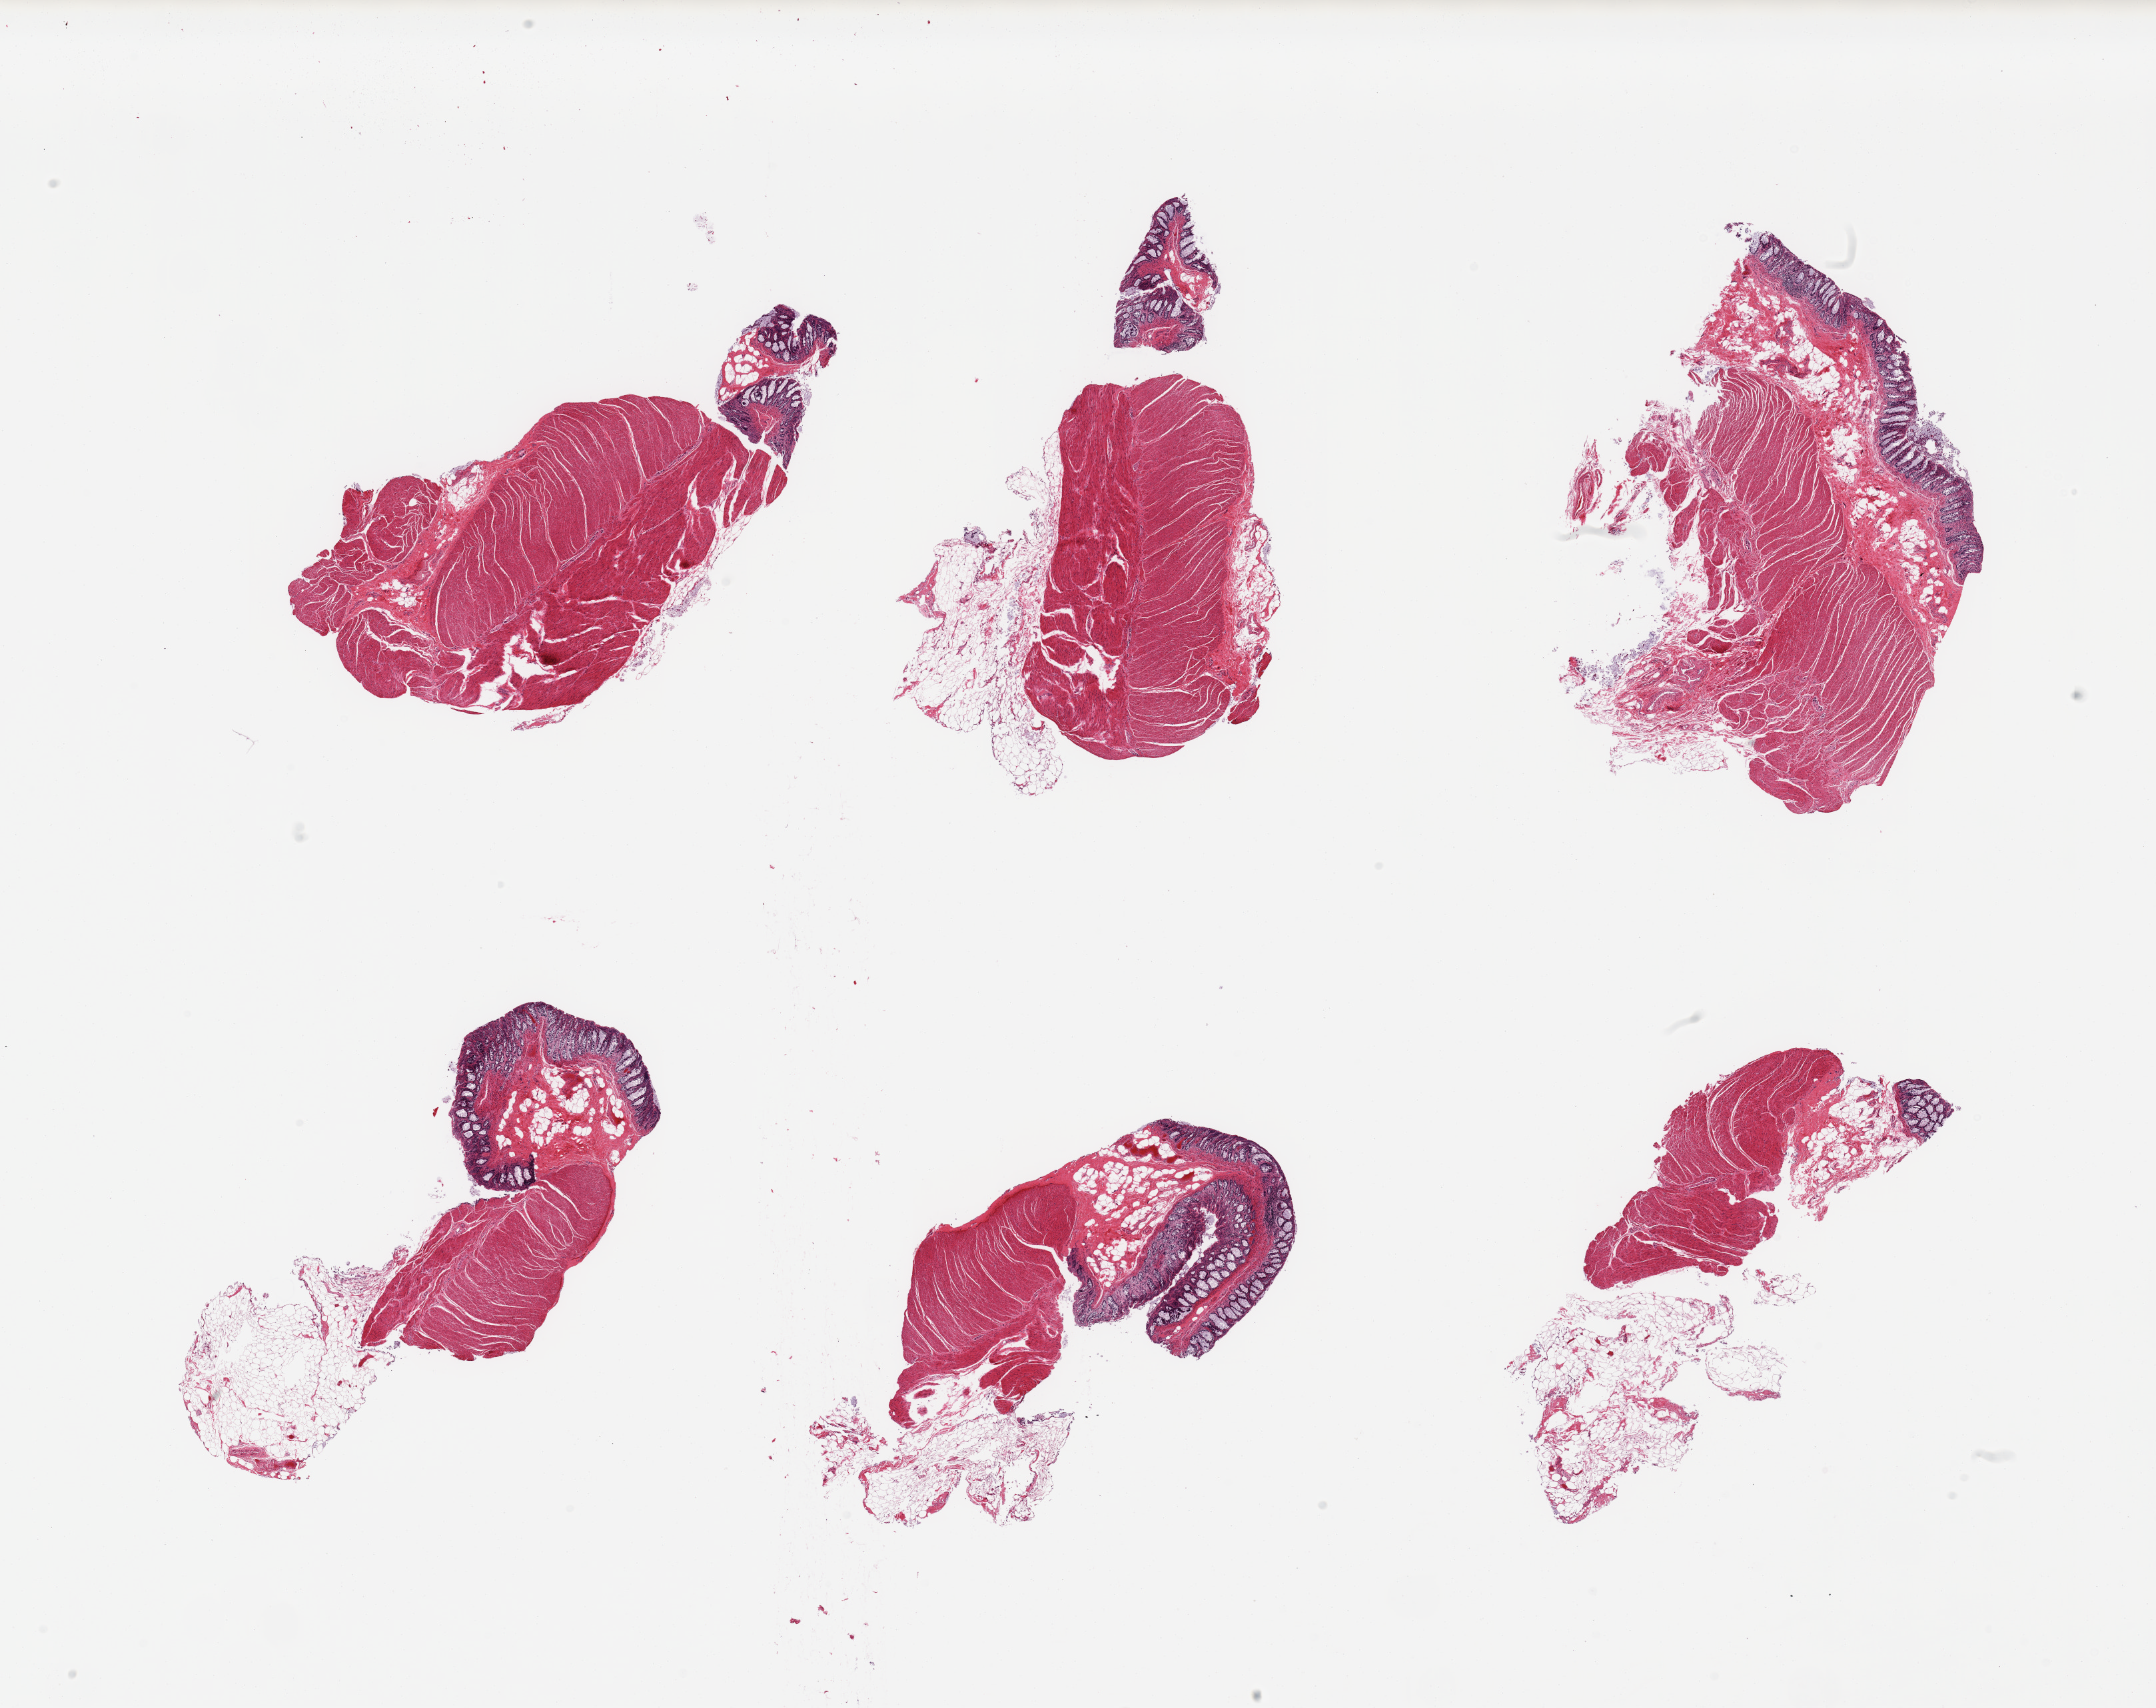
Hematoxylin and eosin (H&E) whole-slide image, low-resolution overview of the scanned area, about 25.6 x 20.3 mm (from a 20x scan); PAXgene-fixed paraffin-embedded (PFPE) section; sampled site (target tissue): sigmoid colon; donor tissue sample. Donor sex: male.
• pathologist's review note for this sample: 6 pieces; muscularis and significant residual mucosa (not target)